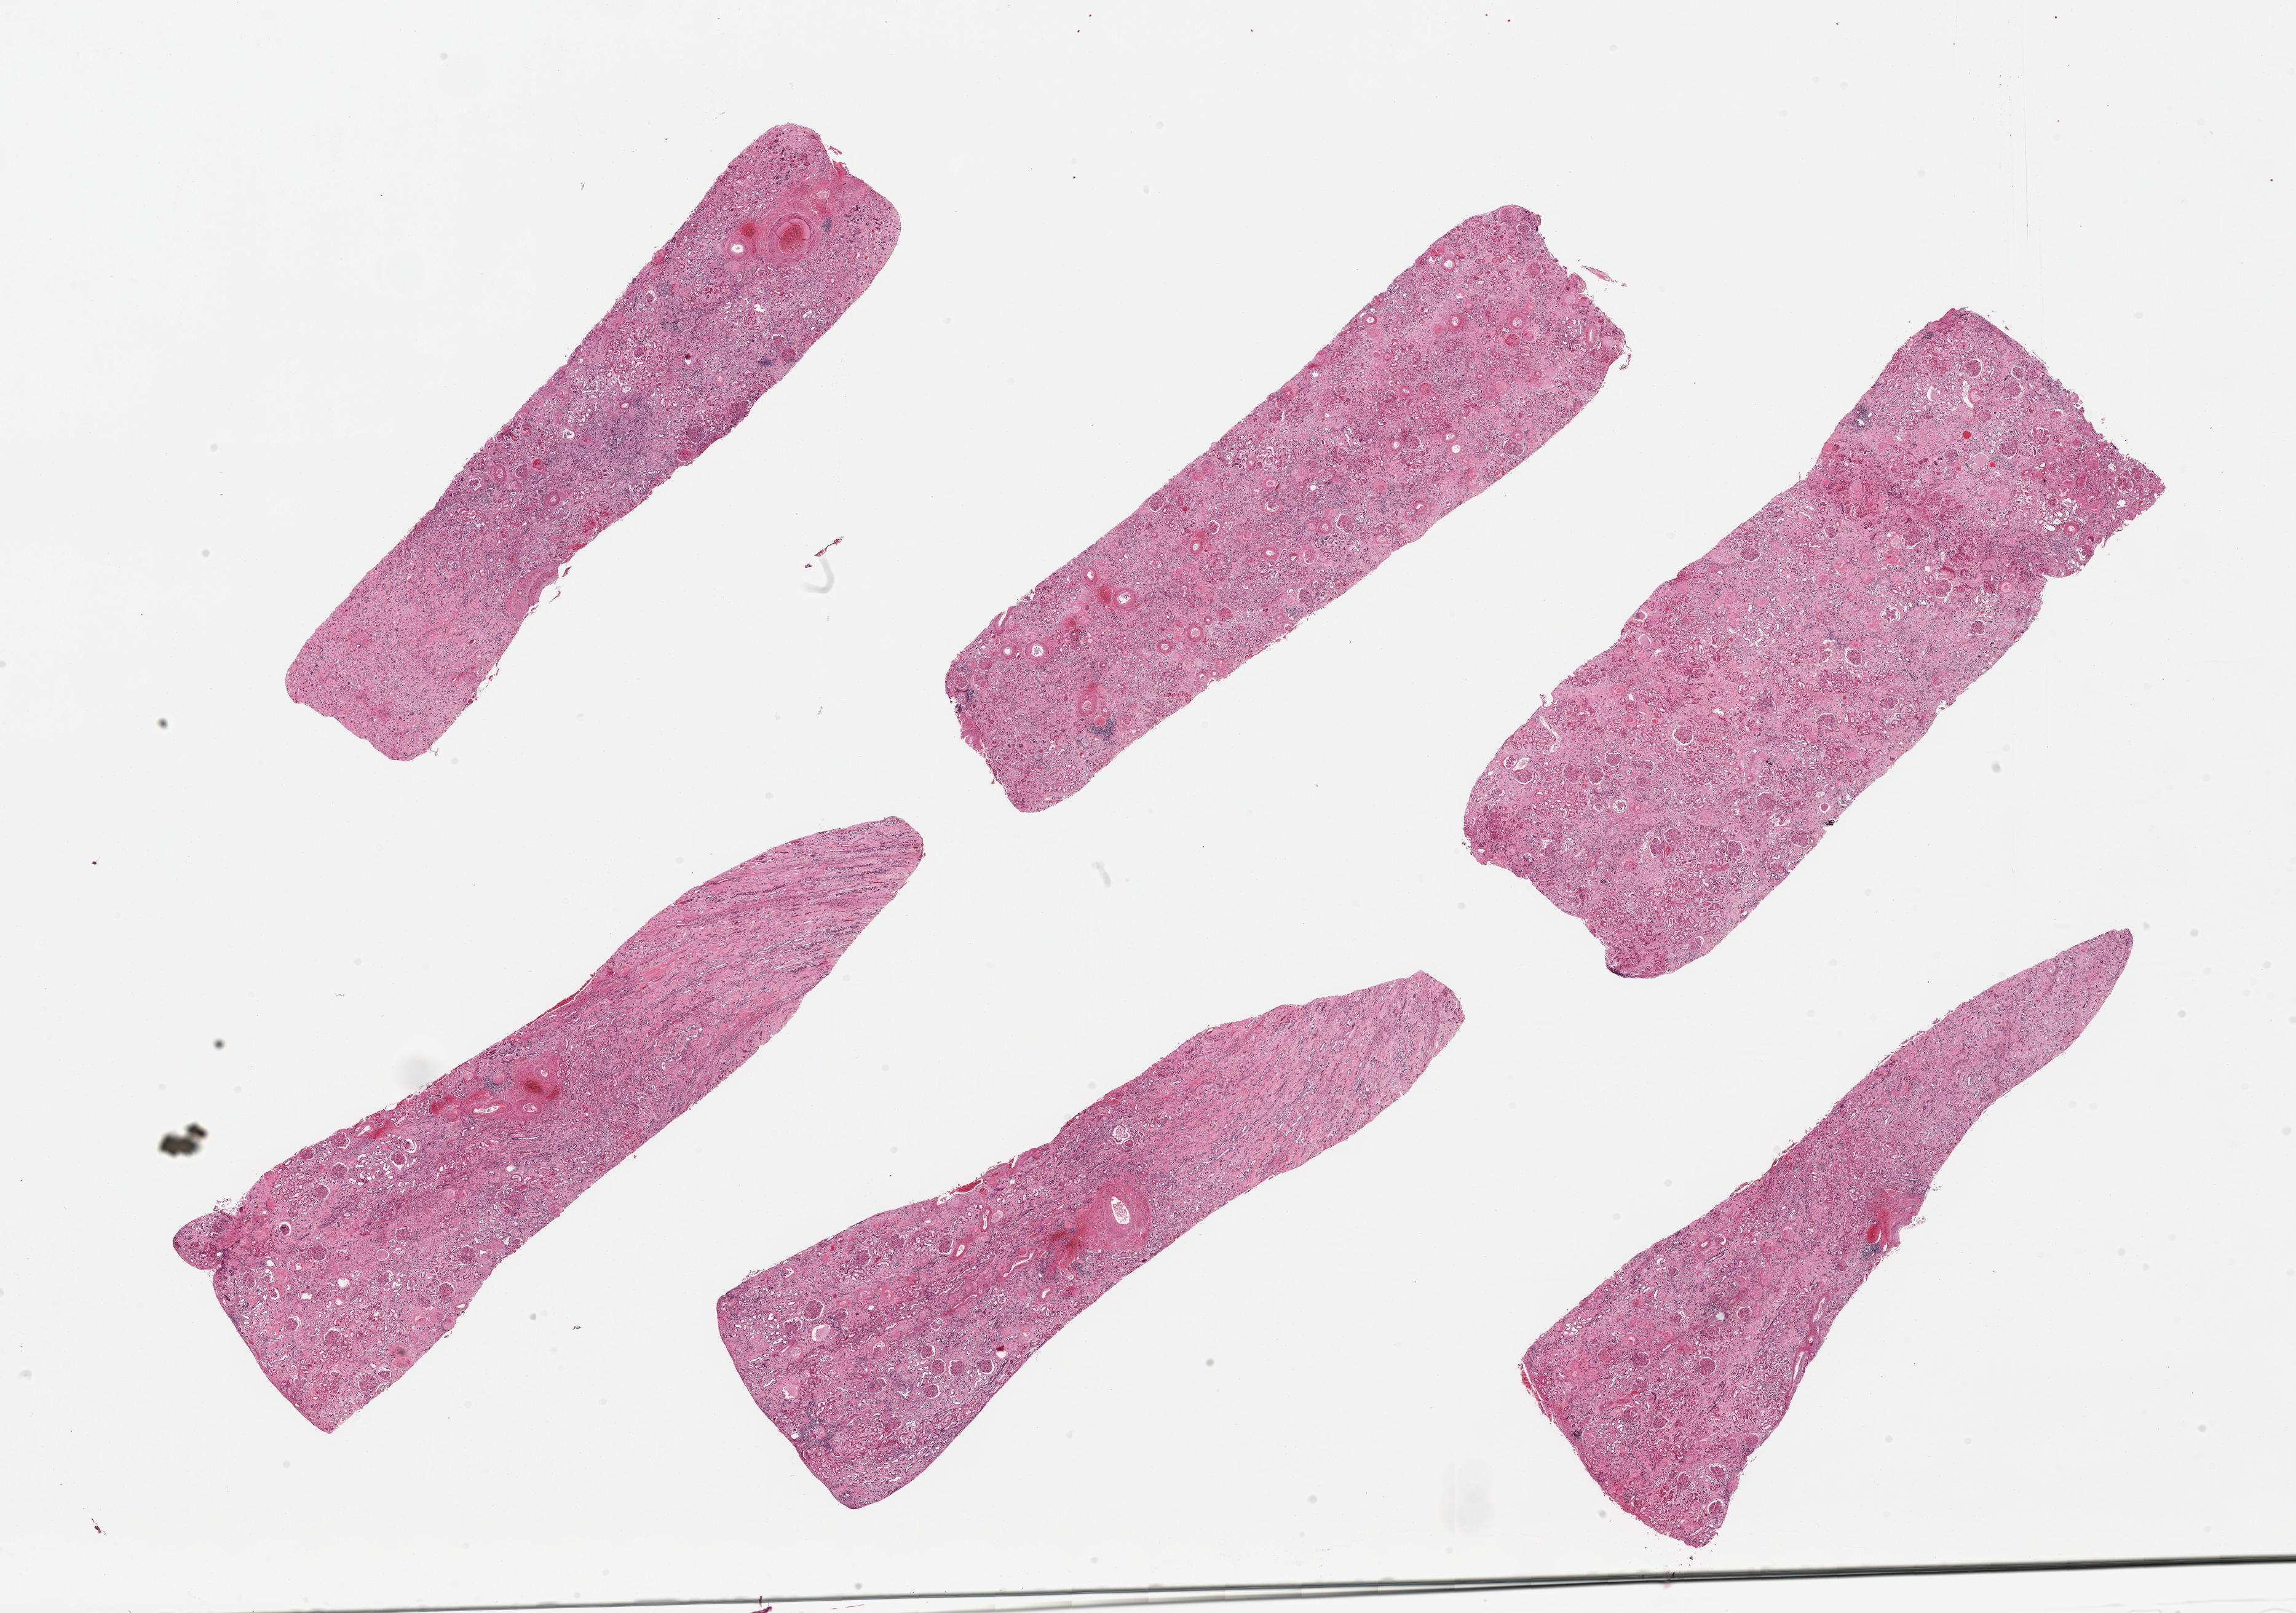
Digitized haematoxylin and eosin-stained section, brightfield, shown as a low-resolution overview of the whole scanned area (about 29.5 x 20.7 mm). PAXgene-fixed, paraffin-embedded tissue. Section of renal cortex (target tissue). Donor tissue sample. Male donor.
Reviewer comment on this tissue sample: 6 pieces, glomeruli present, evidence of advanced glomerulonephritis/interstitial nephritis, moderate-advanced tubular autolysis.